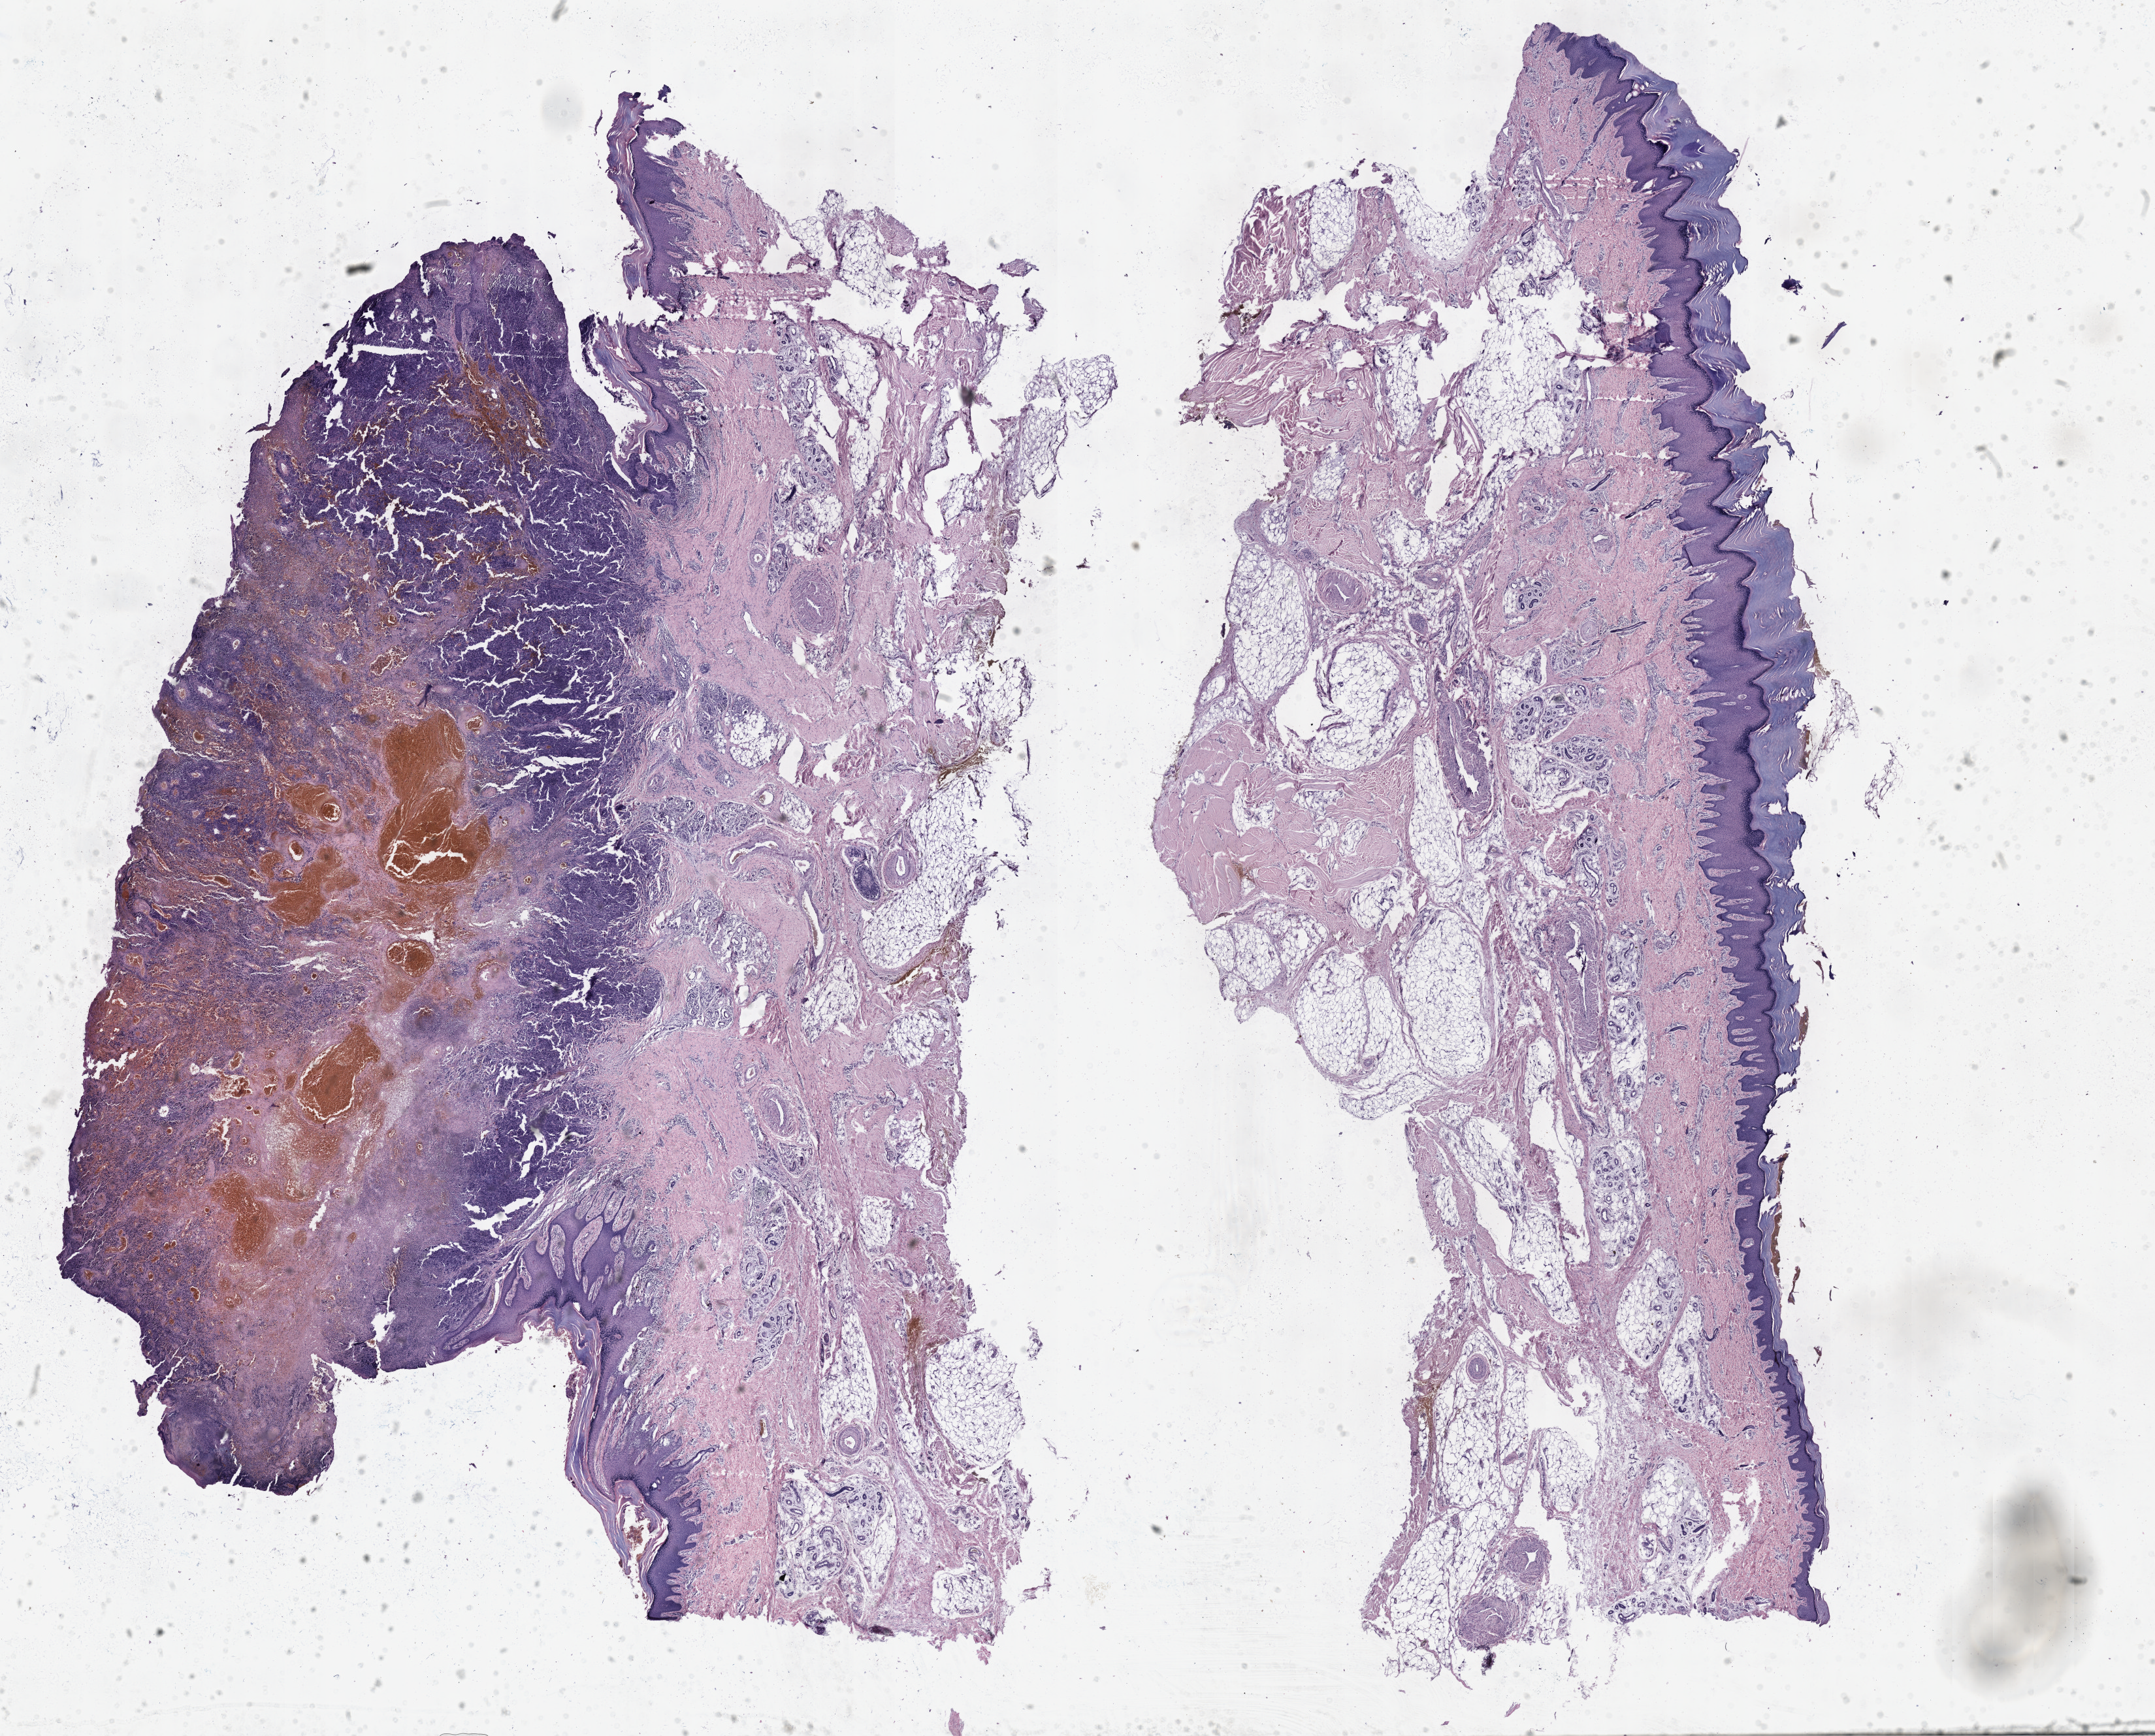
Digitized H&E-stained tissue section (whole slide) — a low-resolution overview of the entire scanned area, about 26.7 x 21.5 mm. Formalin-fixed paraffin-embedded (FFPE) diagnostic section. Primary tumour sample from the skin. Male patient; age at initial diagnosis 81 years.
AJCC pathologic stage: I (7th edition). Histologic diagnosis: Malignant melanoma, NOS.